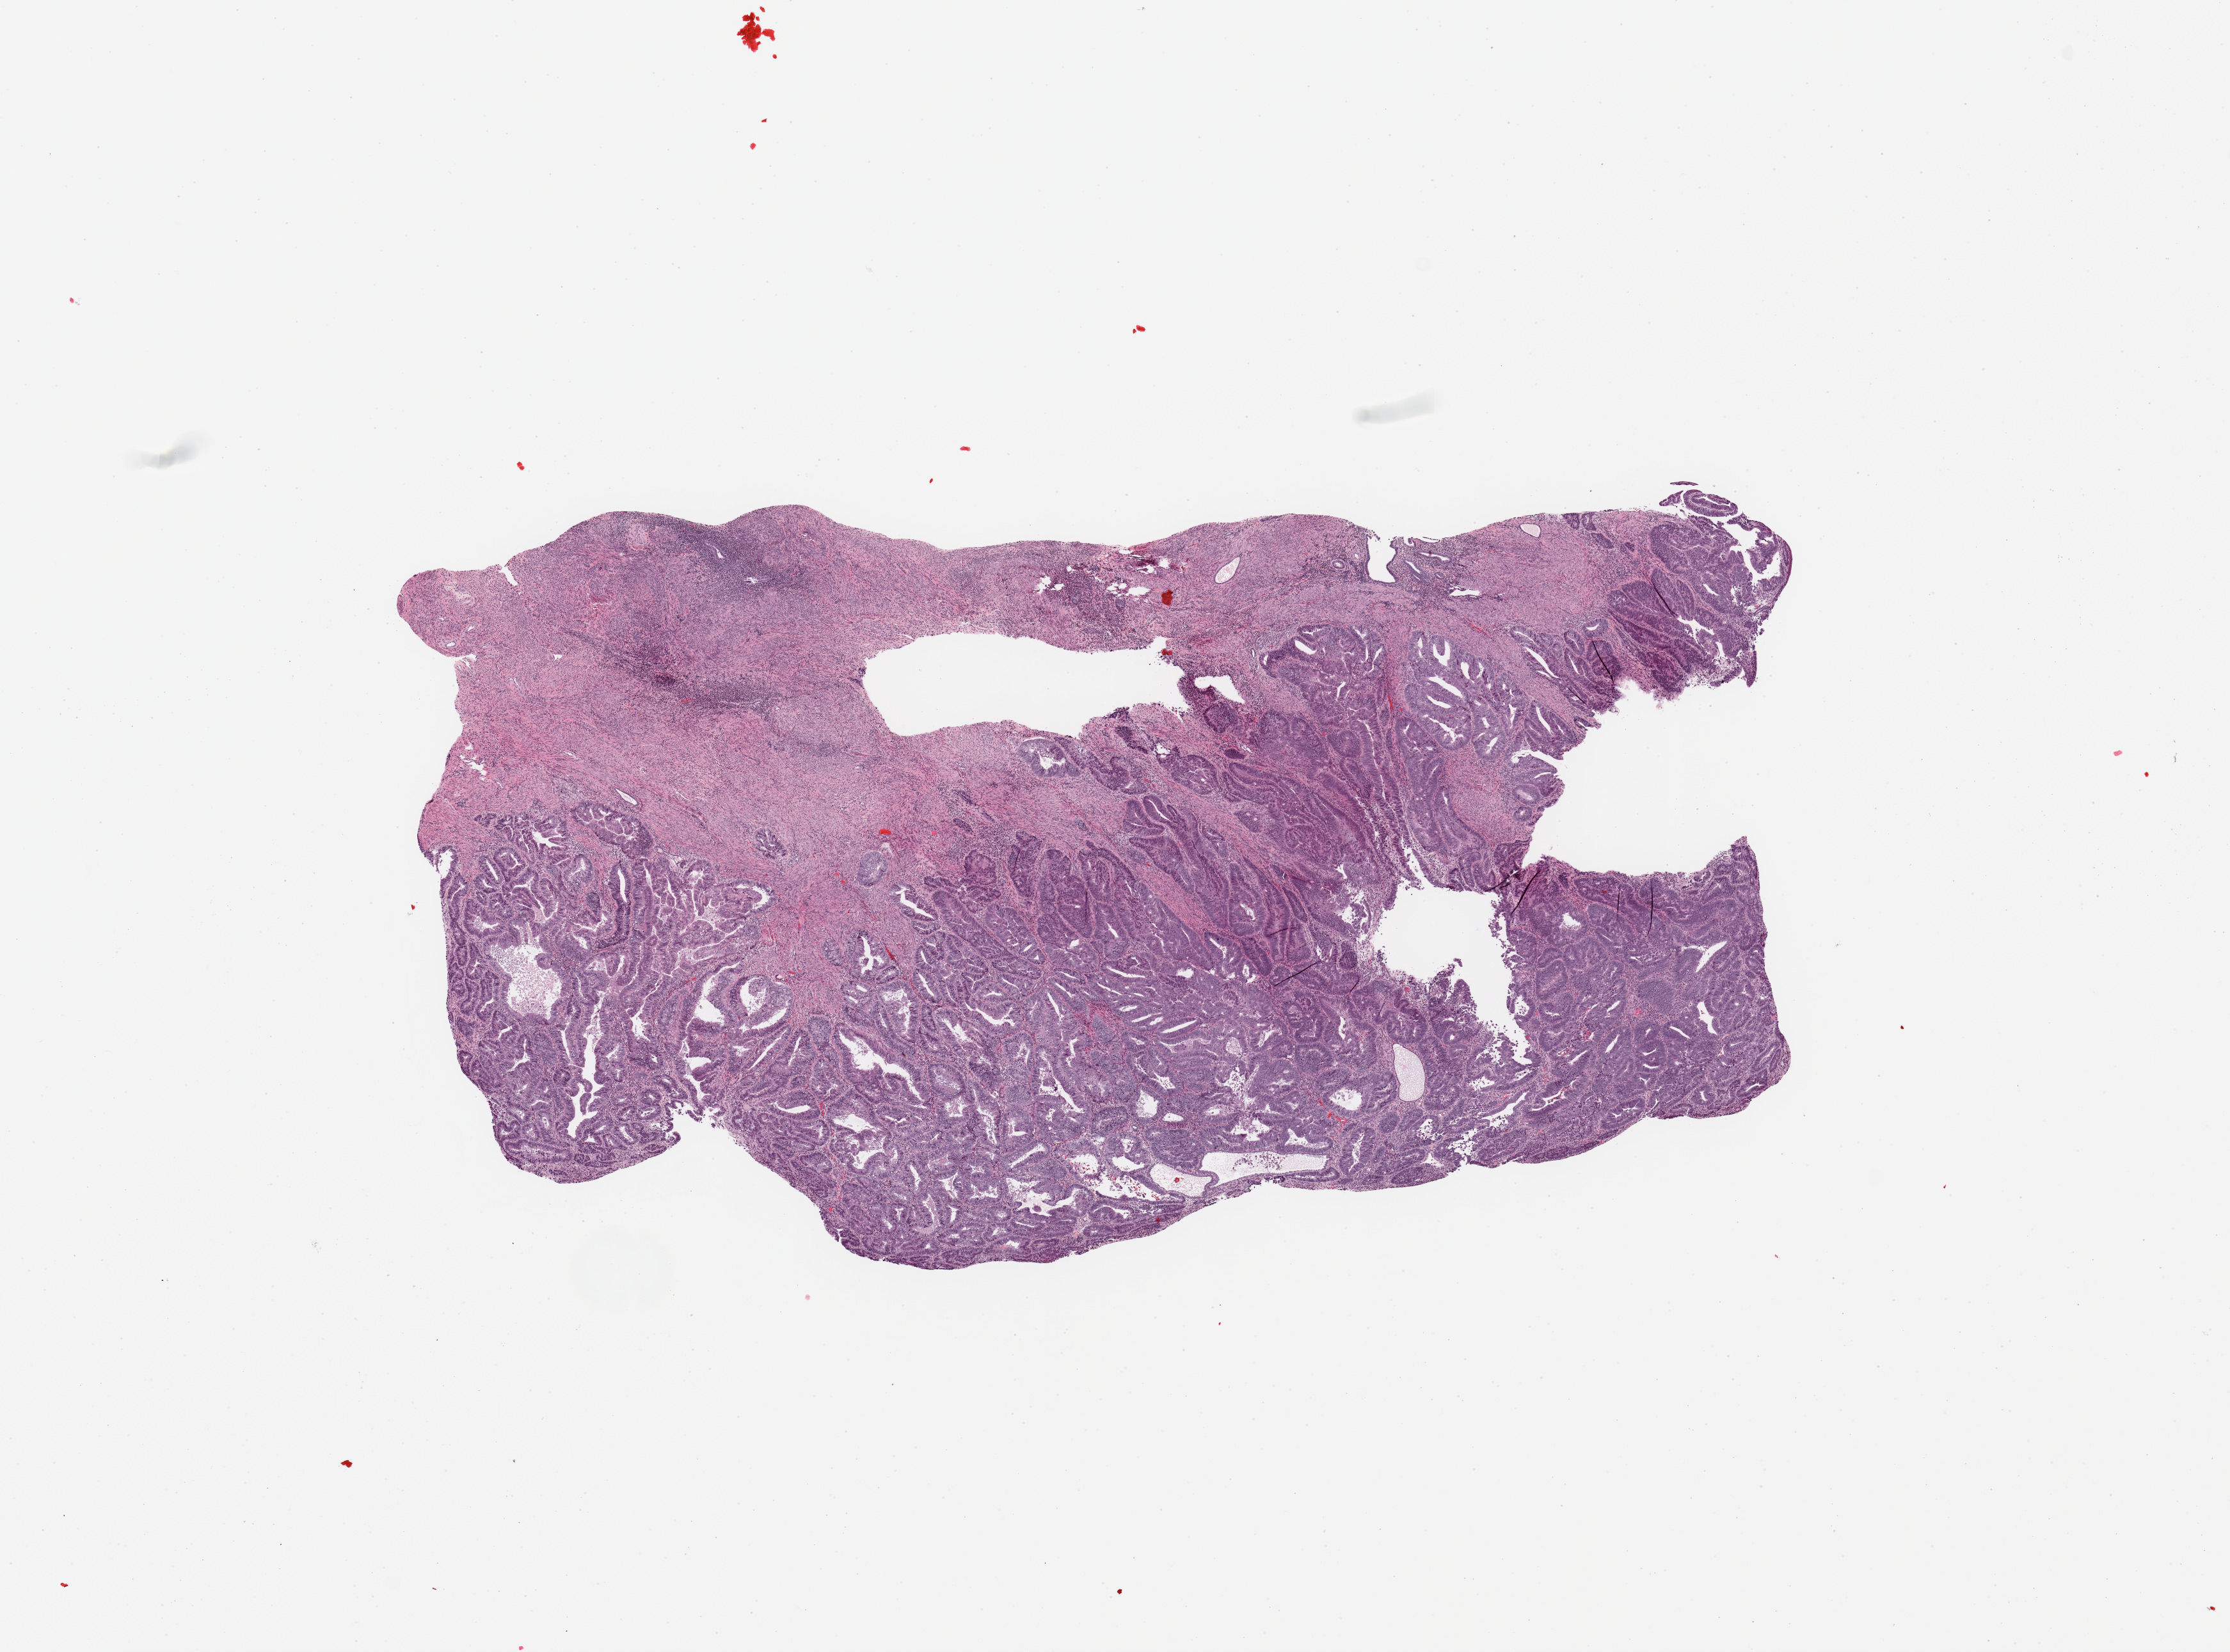
Digitized Hematoxylin and eosin (H&E) stained tissue section (whole slide), whole scanned area (about 13.8 x 10.2 mm, acquisition: 20x scan) shown as a low-resolution overview. Tumour tissue sample, sampled site: uterus. Female, 56 y/o. Histologic grade: G1 (well differentiated). Pathologist review of this section (percent, as recorded): tumour nuclei 80%, necrosis 0%.
AJCC pathologic stage: I. Diagnosis: Endometrioid adenocarcinoma, NOS.